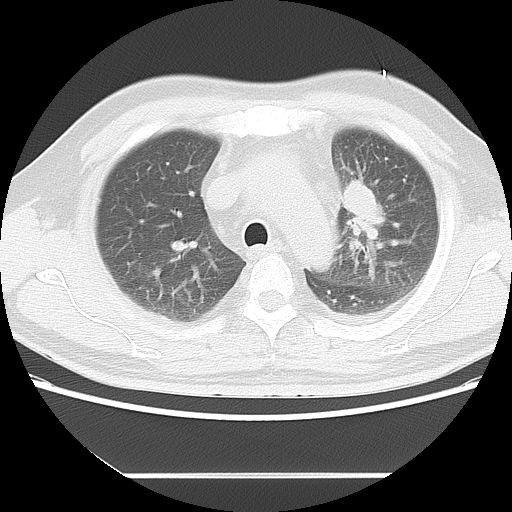
Chest CT, one axial slice. Position 6 of 14 along the scan axis. Reconstruction kernel LUNG. 120 kVp. Lung window (W 1500 / L -600 HU). 512 × 512 image matrix, field of view 350 × 350 mm. Male patient, age 56 years. From the clinical record (not read from this slice): clinical TNM (as recorded): T2 N3 M1.
Structures marked on this image (bounding box drawn by a radiologist):
- lung tumour (recorded histology: adenocarcinoma): box from (x=339, y=171) to (x=389, y=246) px